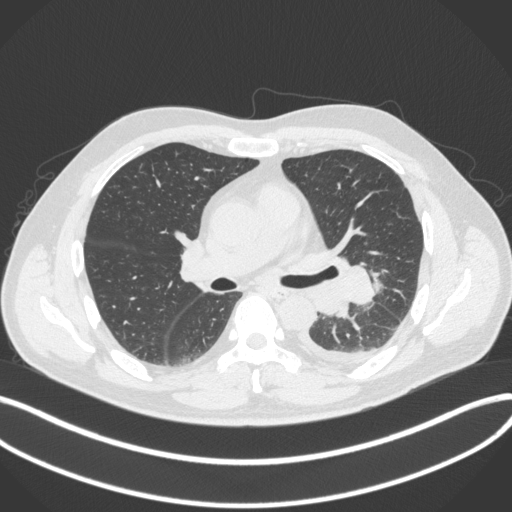
Chest CT, one axial slice; slice 209 of 350 in the series (ordered by position); reconstruction kernel B31f; 120 kVp; lung window (W 1500 / L -600 HU); 1 mm slice thickness; 512 × 512 image matrix. Male patient, age 58 years. Case-level facts recorded for this patient, not image findings: clinical TNM (as recorded): T3 N1 M1b; histopathological grade: G3.
Annotated regions visible in this slice (rectangle marked by the reading radiologist):
- lung tumour (recorded histology: small cell carcinoma): bounding box (x1, y1, x2, y2) in pixels: (305, 259, 377, 313)